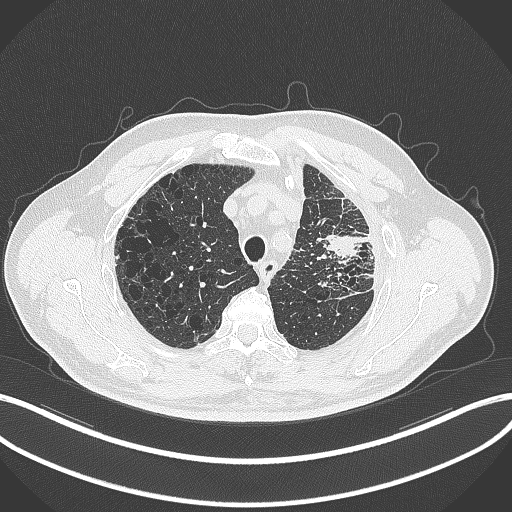
Chest CT, one axial slice. Position 259 of 297 along the scan axis. Reconstruction kernel B70f. 120 kVp. Lung window (W 1500 / L -600 HU). 512 × 512 image matrix. Male patient, age 68 years. Case-level facts recorded for this patient, not image findings: clinical TNM (as recorded): T3 N3 M1.
Annotated regions visible in this slice (bounding box drawn by a radiologist):
- lung tumour (recorded histology: adenocarcinoma): bounding box (x1, y1, x2, y2) in pixels: (319, 229, 367, 267)